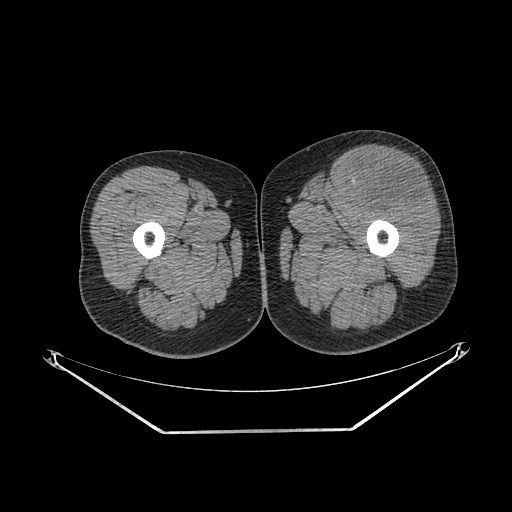
CT of an extremity soft-tissue mass (from a PET/CT study), one axial slice; position 239 of 267 along the scan axis; 140 kVp; soft-tissue window (W 400 / L 40 HU); 512 × 512 image matrix, field of view 500 × 500 mm. Male patient. From the clinical record (not read from this slice): histological type: extraskeletal osteosarcoma; grade: high; site of the primary tumour: thigh.
Outlined on this slice (expert contour drawn on MRI and transferred to this co-registered scan by the dataset authors):
- gross tumour volume (mass): bounding box (x1, y1, x2, y2) in pixels: (352, 160, 430, 211)